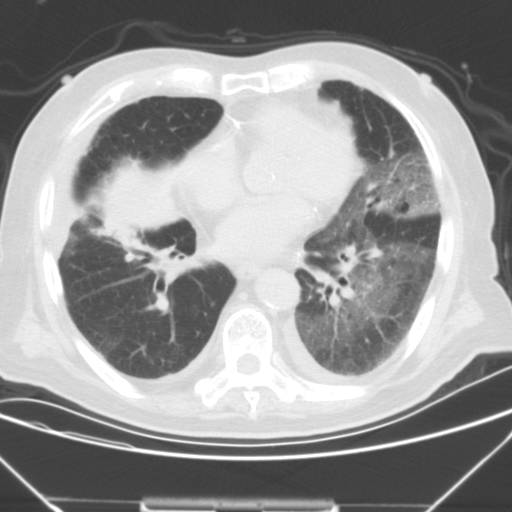
Chest CT, one axial slice; position 13 of 43 along the scan axis; 120 kVp; lung window (W 1500 / L -600 HU); 5 mm slice thickness; 512 × 512 image matrix. Patient: male, 85 years. Case-level facts recorded for this patient, not image findings: clinical TNM (as recorded): T4 N3 M2.
Structures marked on this image (rectangle marked by the reading radiologist):
- lung tumour (recorded histology: squamous cell carcinoma): bounding box <93,162,169,262> (left, top, right, bottom; pixels)